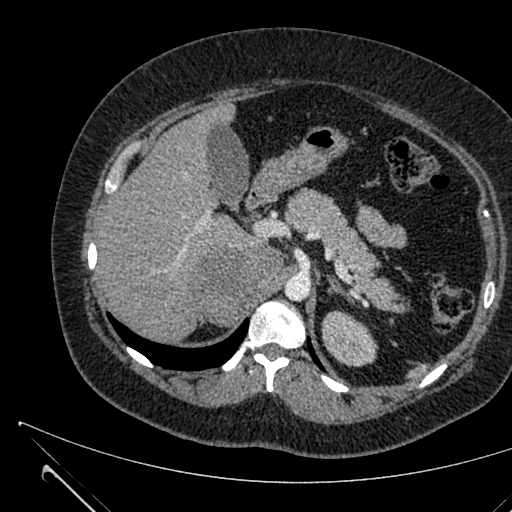
Contrast-enhanced abdominal CT, one axial slice. Position 447 of 731 along the scan axis. 120 kVp. Intravenous contrast given. Soft-tissue window (W 400 / L 40 HU). 1 mm slice thickness. 512 × 512 image matrix, field of view 376 × 376 mm. Female patient, age 36 years. From the clinical record (not read from this slice): diagnosis: adrenocortical carcinoma; tumour side: right adrenal; tumour size at pathology: 10 cm; Ki-67 index: 20 %; stage (as recorded): 4.
Outlined on this slice (semi-automatic segmentation, software-assisted and operator-edited):
- mass: bounding box (x1, y1, x2, y2) in pixels: (197, 247, 282, 324)